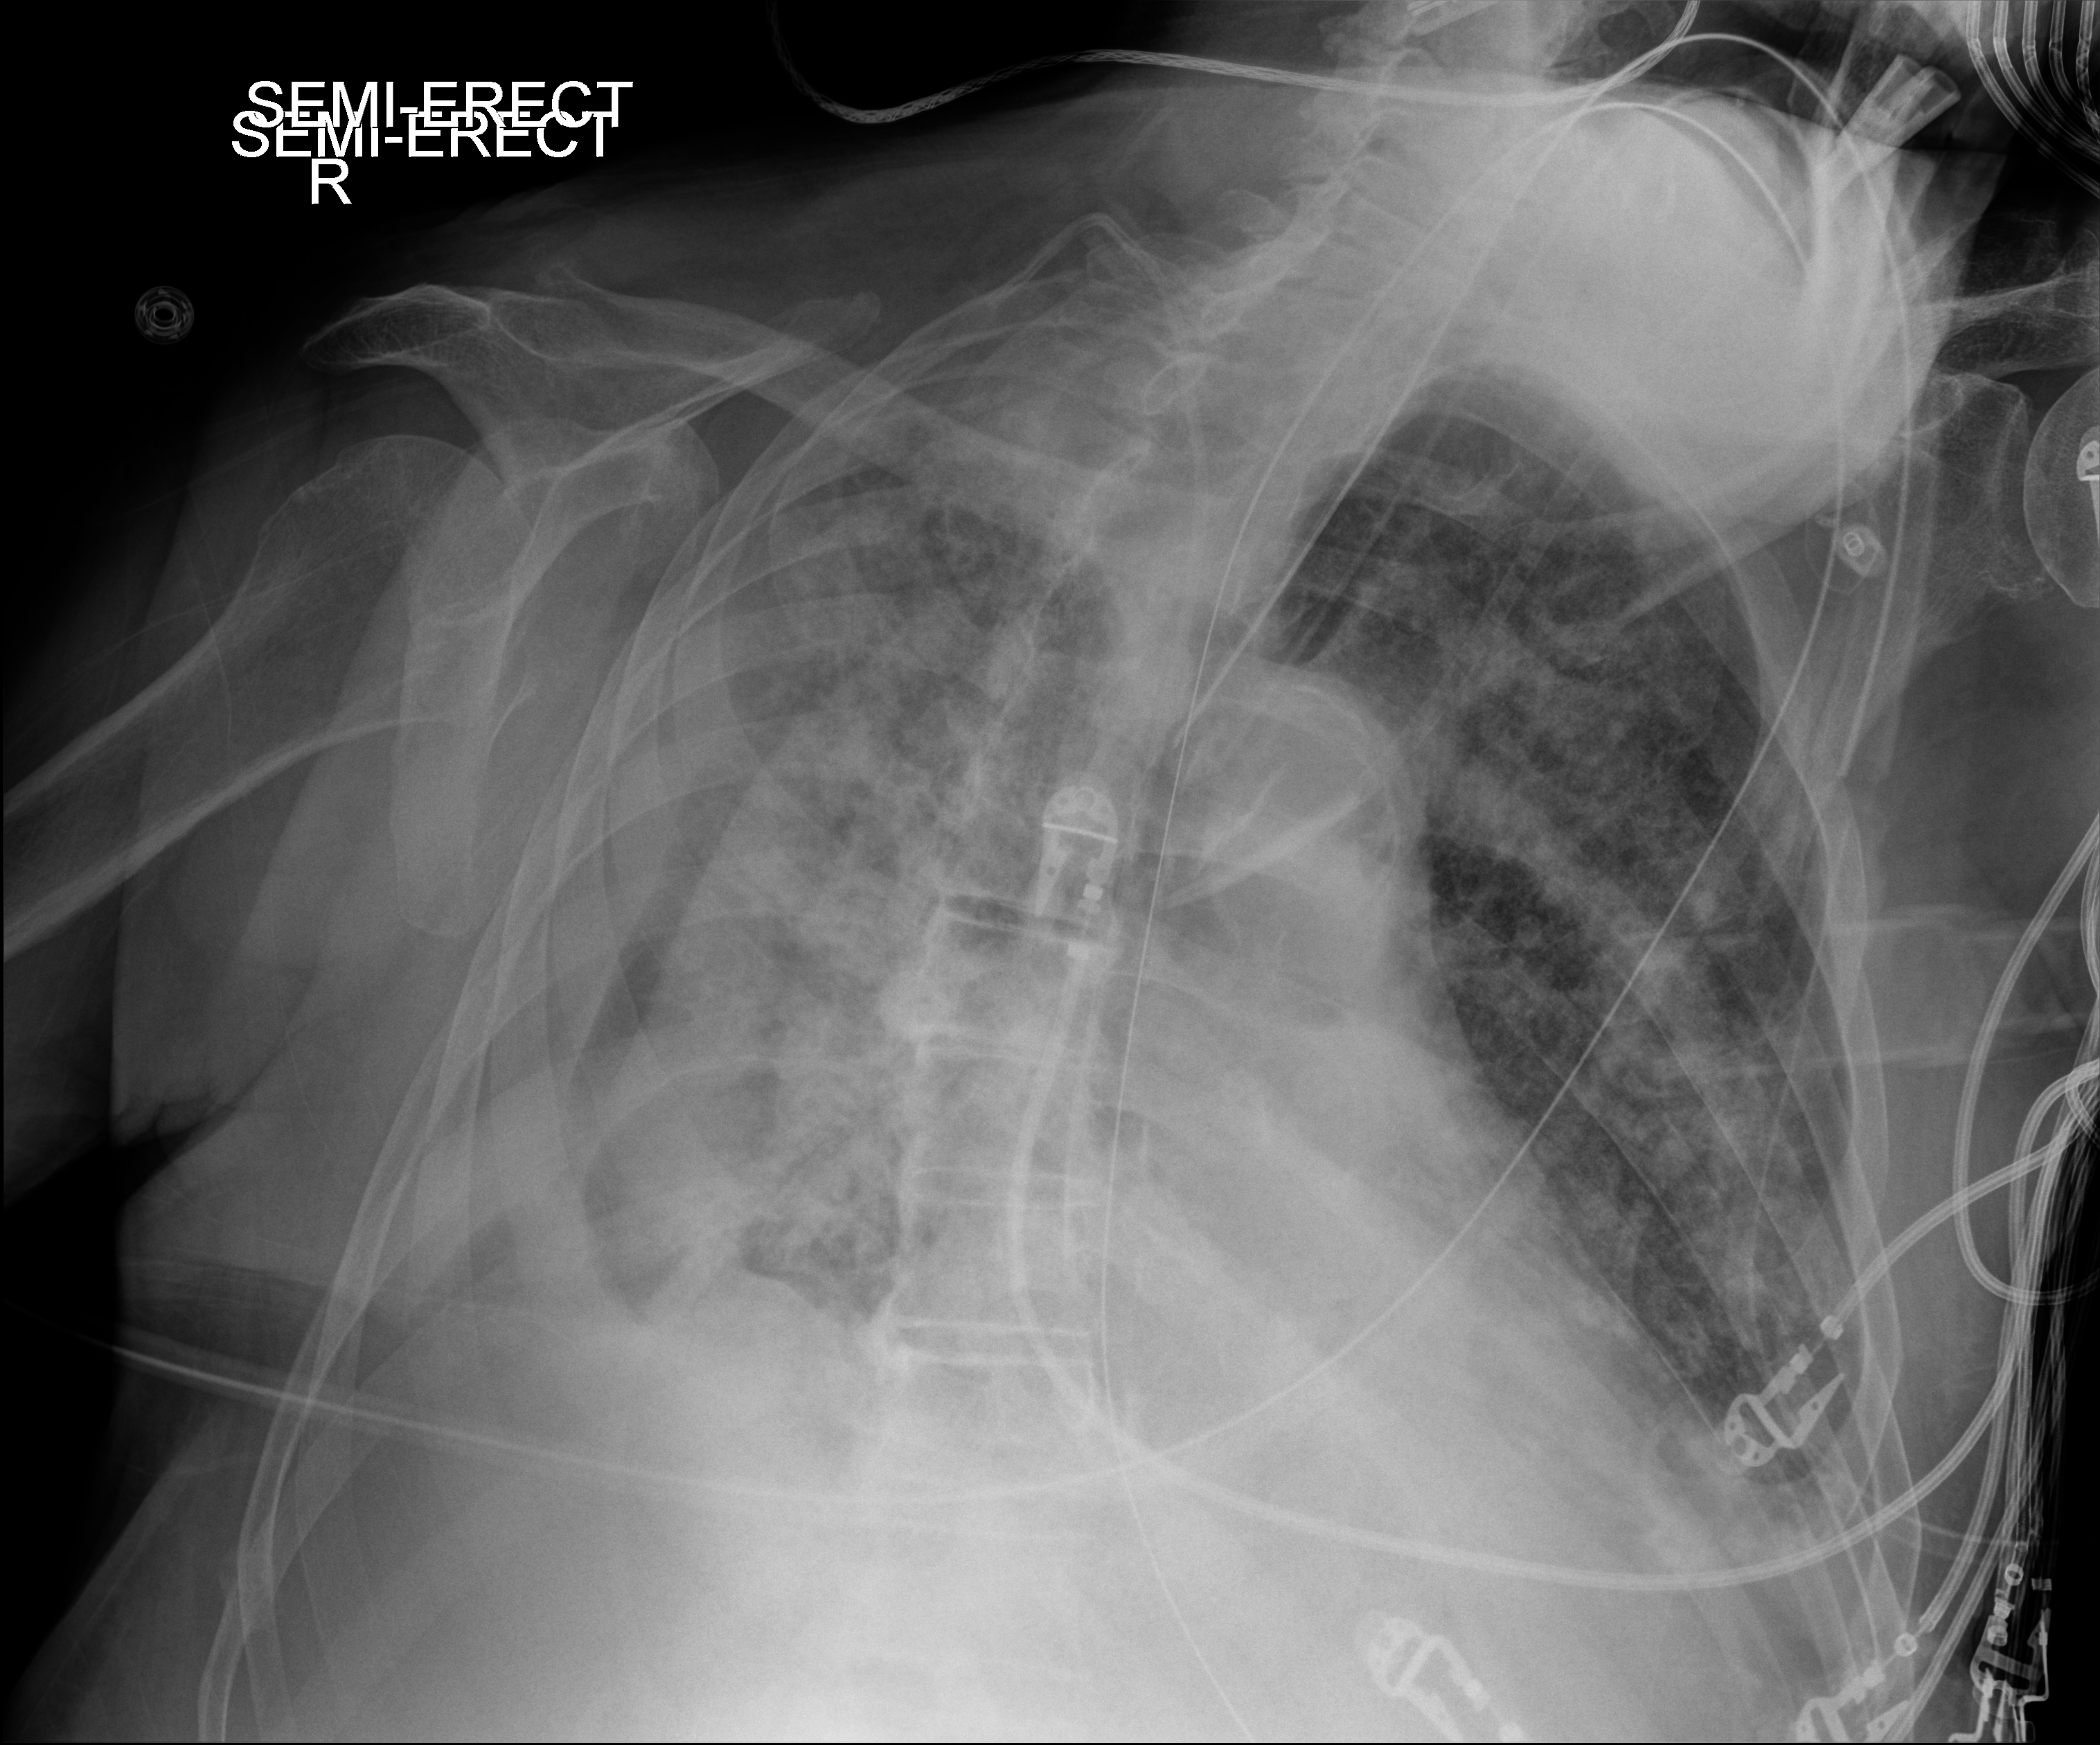
Chest X-ray (portable), anteroposterior (AP) projection. Patient hospitalised with COVID-19; male, aged 75–90 years.
From the hospital-stay record, not from the radiograph (when in the stay this image was taken is not recorded): other chronic lung disease (admission record): no.